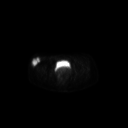
FDG PET of an extremity soft-tissue mass (from a PET/CT study), one axial slice; slice 66 of 267 in the series (ordered by position); 3.27 mm slice thickness; 128 × 128 image matrix. Female patient, age 34 years. From the clinical record (not read from this slice): histological type: synovial sarcoma; grade: intermediate; site of the primary tumour: right thigh.
Outlined on this slice (expert contour drawn on MRI and transferred to this co-registered scan by the dataset authors):
- gross tumour volume including surrounding oedema: bounding box [x1, y1, x2, y2] px = [30, 57, 40, 68]
- gross tumour volume (mass): [30, 57, 40, 67]